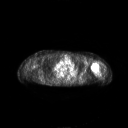
FDG PET of an extremity soft-tissue mass (from a PET/CT study), one axial slice. Slice 181 of 267 in the series (ordered by position). 3.27 mm slice thickness. 128 × 128 image matrix. Female patient, age 83 years. Case-level facts recorded for this patient, not image findings: histological type: pleiomorphic leiomyosarcoma; grade: high; site of the primary tumour: left biceps.
Outlined on this slice (expert contour drawn on MRI and transferred to this co-registered scan by the dataset authors):
- gross tumour volume including surrounding oedema: bounding box (x1, y1, x2, y2) in pixels: (91, 63, 99, 74)
- gross tumour volume (mass): (91, 63, 99, 73)